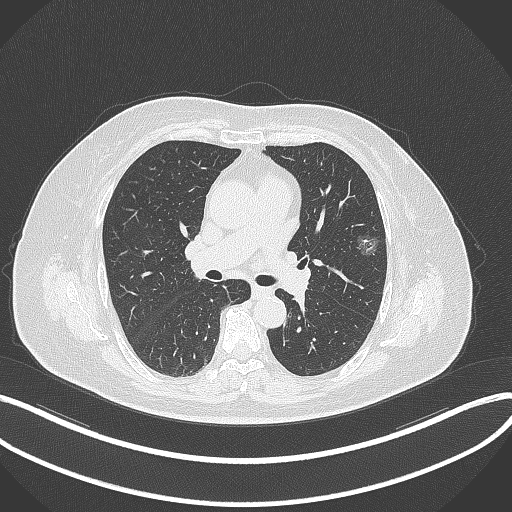
Chest CT, one axial slice; slice 210 of 315 in the series (ordered by position); reconstruction kernel B70f; lung window (W 1500 / L -600 HU); 512 × 512 image matrix, field of view 400 × 400 mm. Female patient, age 76 years. From the clinical record (not read from this slice): clinical TNM (as recorded): T1b N0 M0; histopathological grade: G1-2.
Annotated regions visible in this slice (rectangle marked by the reading radiologist):
- lung tumour (recorded histology: adenocarcinoma): bounding box <351,226,381,259> (left, top, right, bottom; pixels)